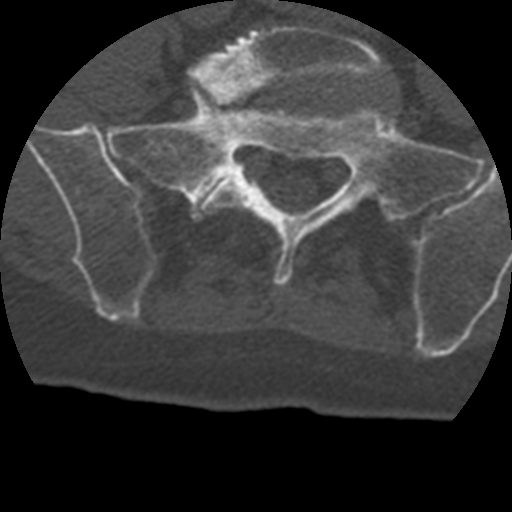
CT including the spine, one axial slice; slice 30 of 399 in the series (ordered by position); reconstruction kernel STANDARD; 120 kVp; bone window (W 1800 / L 400 HU); 1.25 mm slice thickness; 512 × 512 image matrix. Patient age 69 years. Case-level facts recorded for this patient, not image findings: primary cancer: prostate.
Annotated regions visible in this slice (semi-automatic segmentation, software-assisted and operator-edited):
- L5 vertebra: bounding box (x1, y1, x2, y2) in pixels: (189, 25, 389, 212)